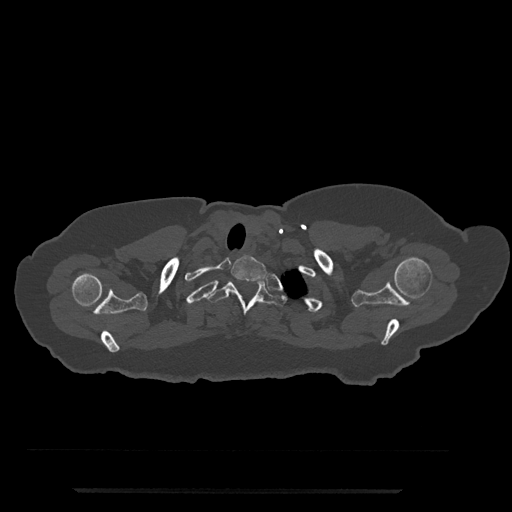
CT including the spine, one axial slice. Slice 687 of 797 in the series (ordered by position). Reconstruction kernel Br40s/3. 120 kVp. Bone window (W 1800 / L 400 HU). 0.5 mm slice thickness. 512 × 512 image matrix, field of view 440 × 440 mm. Female patient, age 51 years. Case-level facts recorded for this patient, not image findings: primary cancer: neuro; vertebrae with lytic lesions (as recorded): T8.
Structures marked on this image (semi-automatic segmentation, software-assisted and operator-edited):
- T1 vertebra: bounding box <231,255,267,282> (left, top, right, bottom; pixels)
- T2 vertebra: <206,275,286,315>